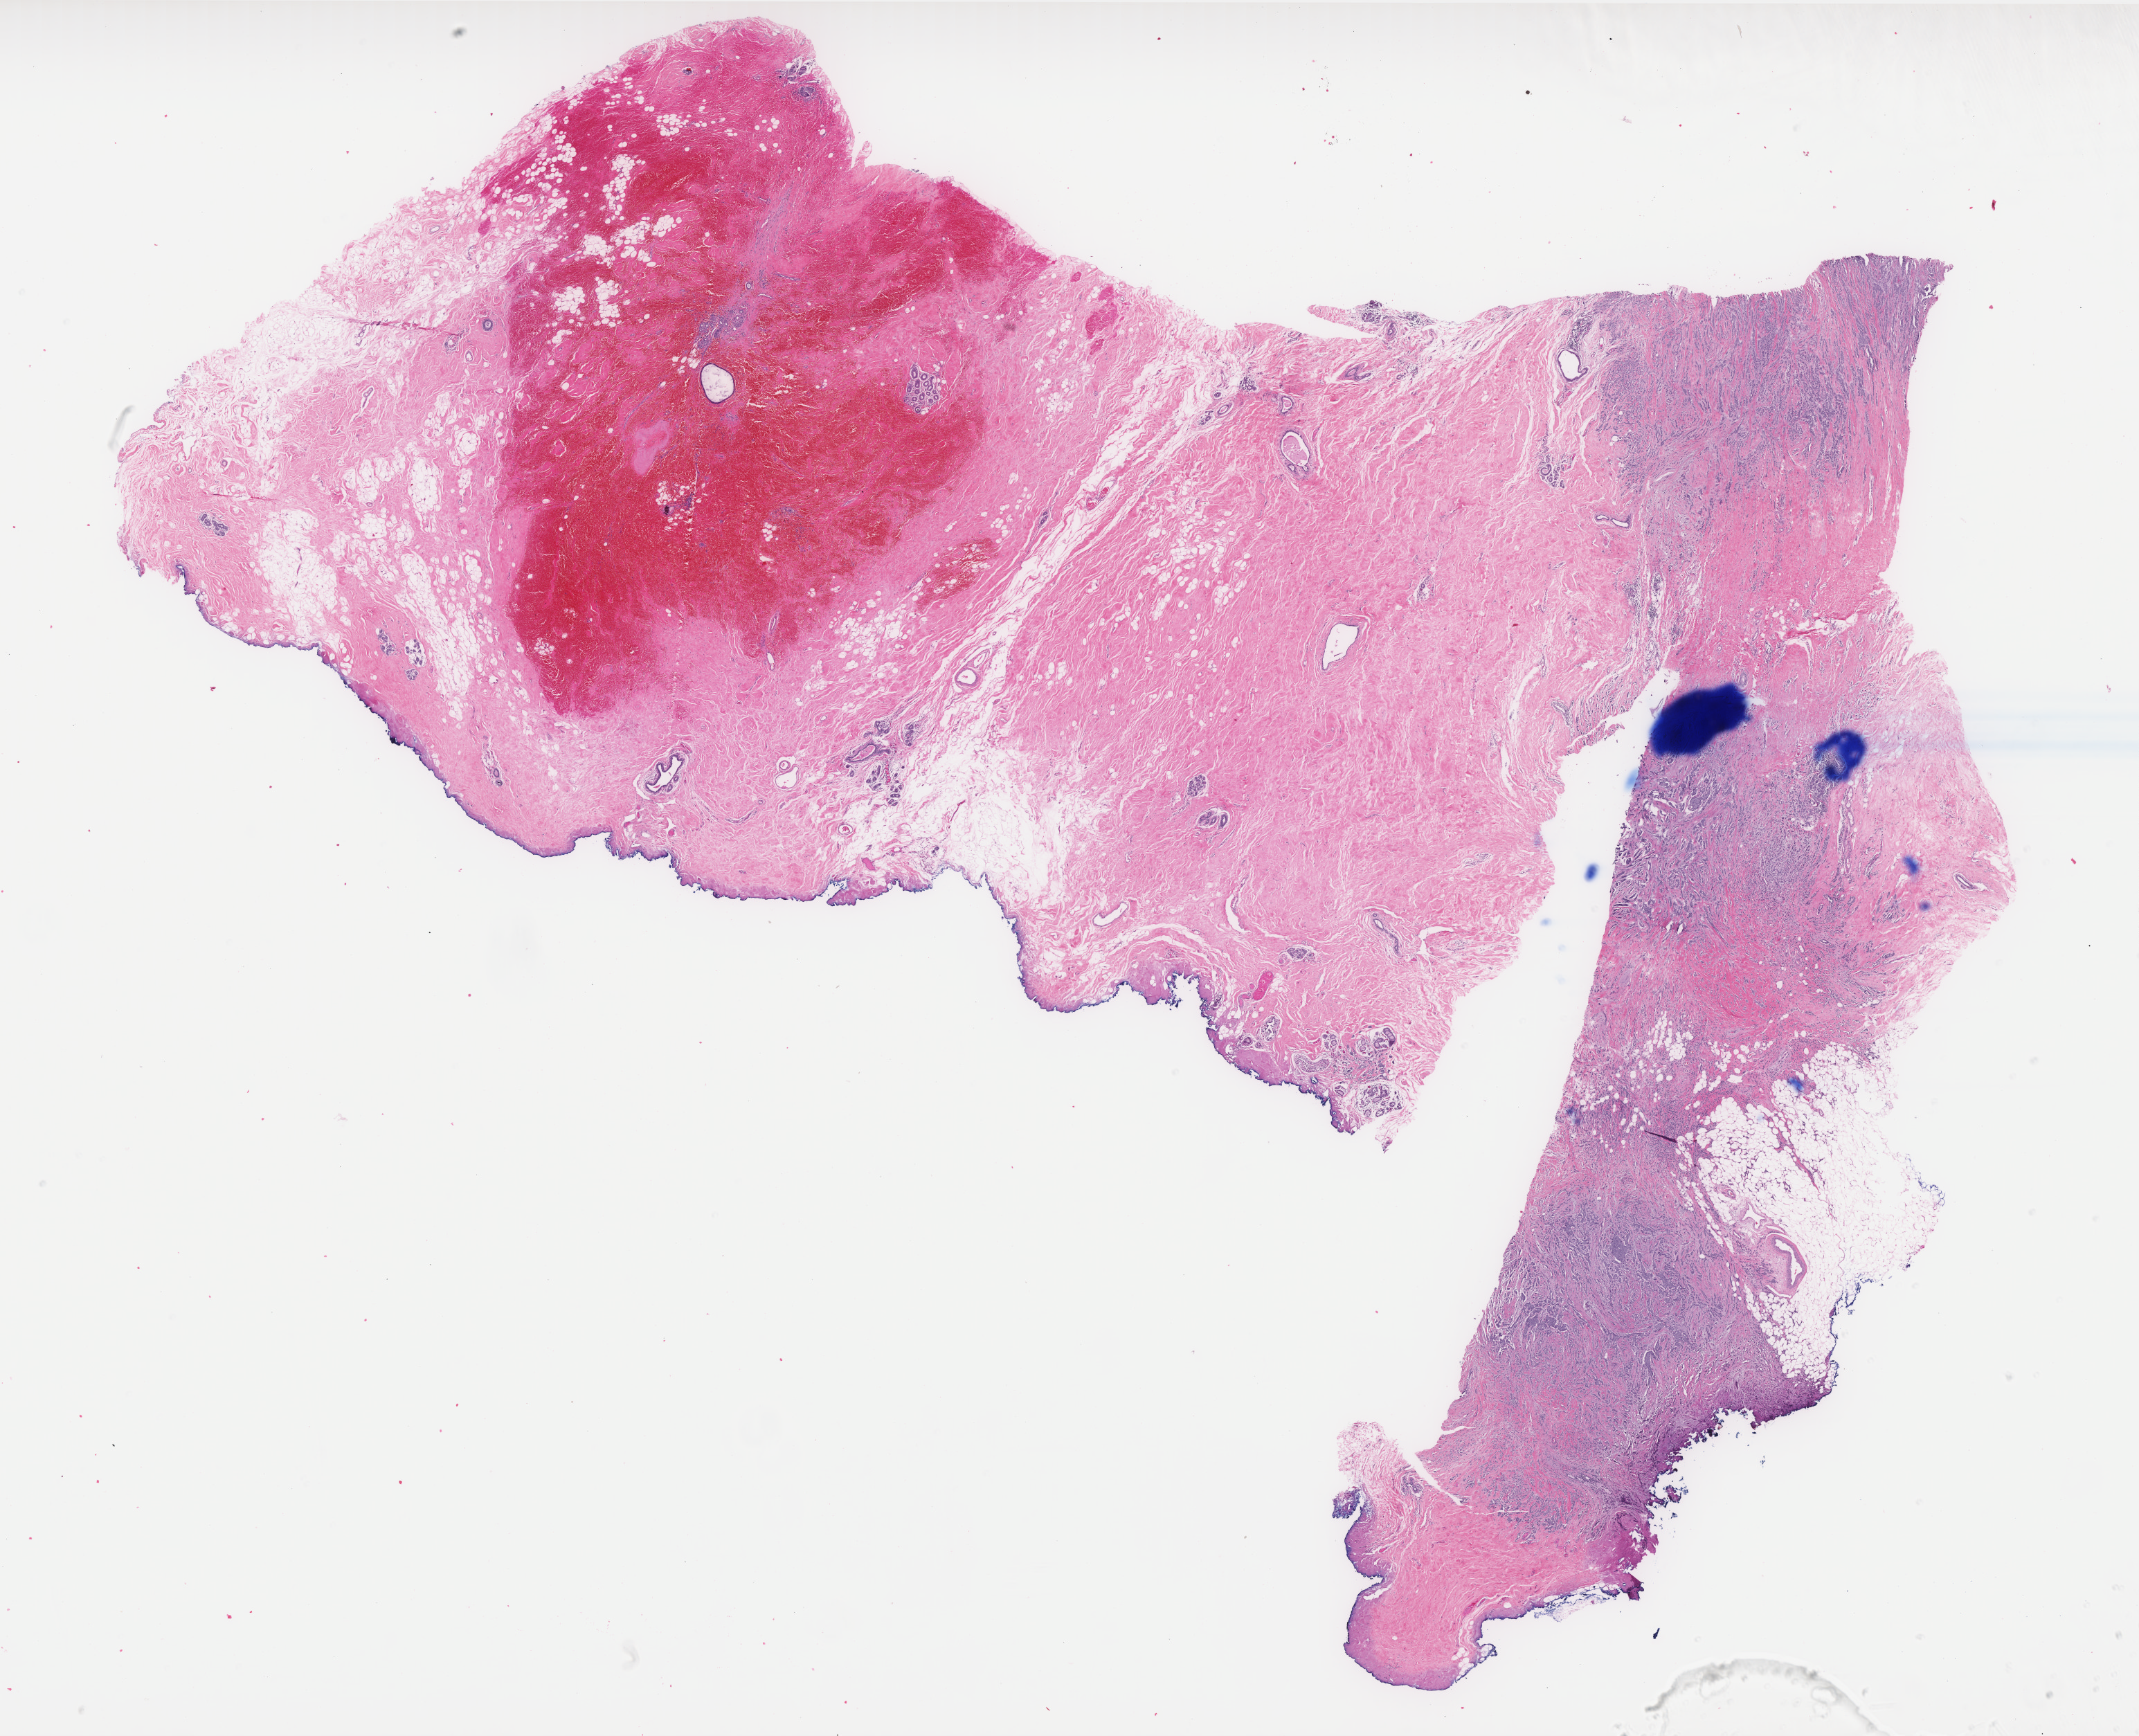
Whole-slide histology image, Hematoxylin and eosin (H&E) stained, low-resolution overview of the scanned area, about 24.8 x 20.1 mm; formalin-fixed paraffin-embedded (FFPE) diagnostic section; sample: primary tumour, breast. Female patient; age at initial diagnosis 60 years.
• AJCC pathologic stage: IA
• pathologic diagnosis: Infiltrating duct carcinoma, NOS